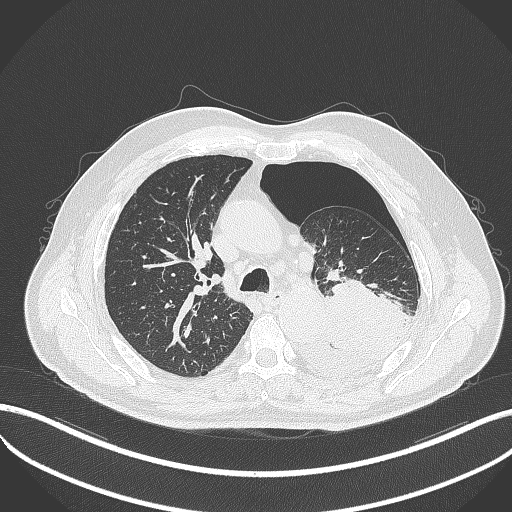
Chest CT, one axial slice. Position 351 of 464 along the scan axis. Reconstruction kernel B70f. Lung window (W 1500 / L -600 HU). 1 mm slice thickness. 512 × 512 image matrix. Male patient, age 76 years. From the clinical record (not read from this slice): clinical TNM (as recorded): T3 N0 M1b.
Structures marked on this image (rectangle marked by the reading radiologist):
- lung tumour (recorded histology: adenocarcinoma): box from (x=321, y=277) to (x=405, y=352) px